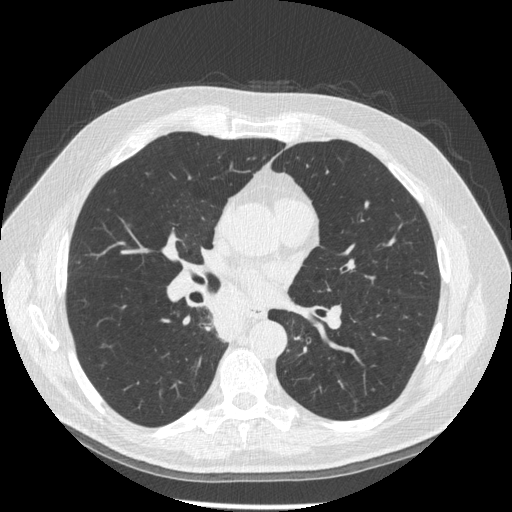
Chest CT (low-dose screening protocol), one axial image. Third screening round (two years after baseline). Lung window (W 1500 / L -600 HU). 1.25 mm slice thickness. Slice 86 of 181 in the series. Male participant, aged 61 years at enrolment.
• Expert-annotated lung lesion, box from (x=203, y=298) to (x=255, y=348) px.
• No non-calcified nodule or mass ≥4 mm was recorded by the screening reader at this exam.
• Later outcome: lung cancer diagnosed 10 days after this screen — squamous cell carcinoma, keratinizing, NOS, right lower lobe, stage IIIB (AJCC 6th edition), 40 mm at pathology.